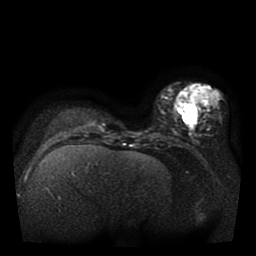
Breast MRI, one axial slice. Position 14 of 41 along the scan axis. Diffusion-weighted series; image 2 of 4 stored at this slice position (different b-values; order by instance number). 1.5 T. 256 × 256 image matrix, field of view 330 × 330 mm. Female patient.
Annotated regions visible in this slice (outlined manually by an expert reader):
- tumour on diffusion-weighted imaging: bounding box (x1, y1, x2, y2) in pixels: (185, 105, 197, 122)